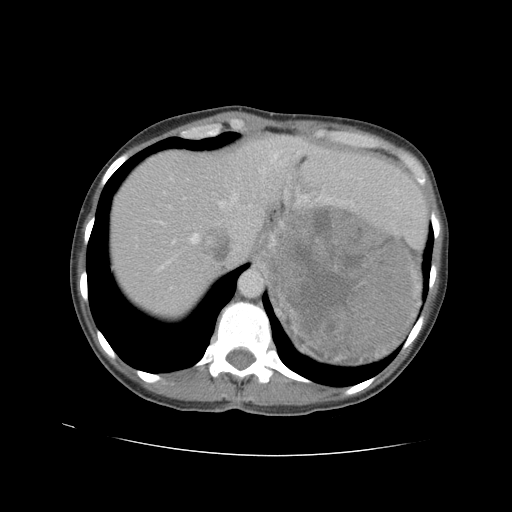
Contrast-enhanced abdominal CT, one axial slice. Position 77 of 90 along the scan axis. Reconstruction kernel STANDARD. 120 kVp. Intravenous contrast given. Soft-tissue window (W 400 / L 40 HU). 5 mm slice thickness. 512 × 512 image matrix. Female patient. From the clinical record (not read from this slice): diagnosis: adrenocortical carcinoma; tumour side: left adrenal; tumour size at pathology: 18 cm; Ki-67 index: 11 %; stage (as recorded): 3.
Structures marked on this image (semi-automatic segmentation, software-assisted and operator-edited):
- mass: bounding box [x1, y1, x2, y2] px = [272, 208, 413, 357]